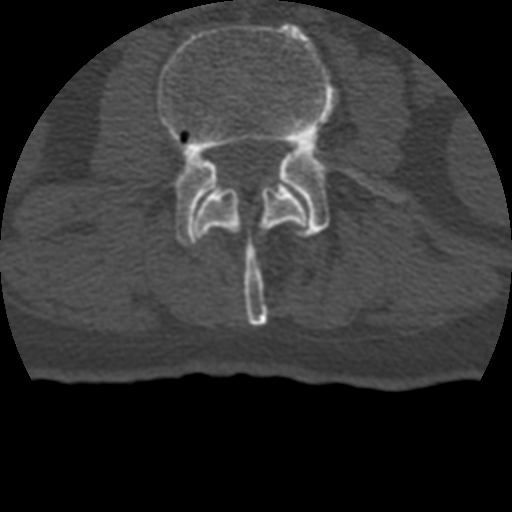
CT including the spine, one axial slice; position 100 of 399 along the scan axis; reconstruction kernel STANDARD; bone window (W 1800 / L 400 HU); 1.25 mm slice thickness; 512 × 512 image matrix. Patient age 69 years. From the clinical record (not read from this slice): primary cancer: prostate.
Structures marked on this image (semi-automatic segmentation, software-assisted and operator-edited):
- L2 vertebra: bounding box <194,186,308,326> (left, top, right, bottom; pixels)
- L3 vertebra: <157,23,404,244>